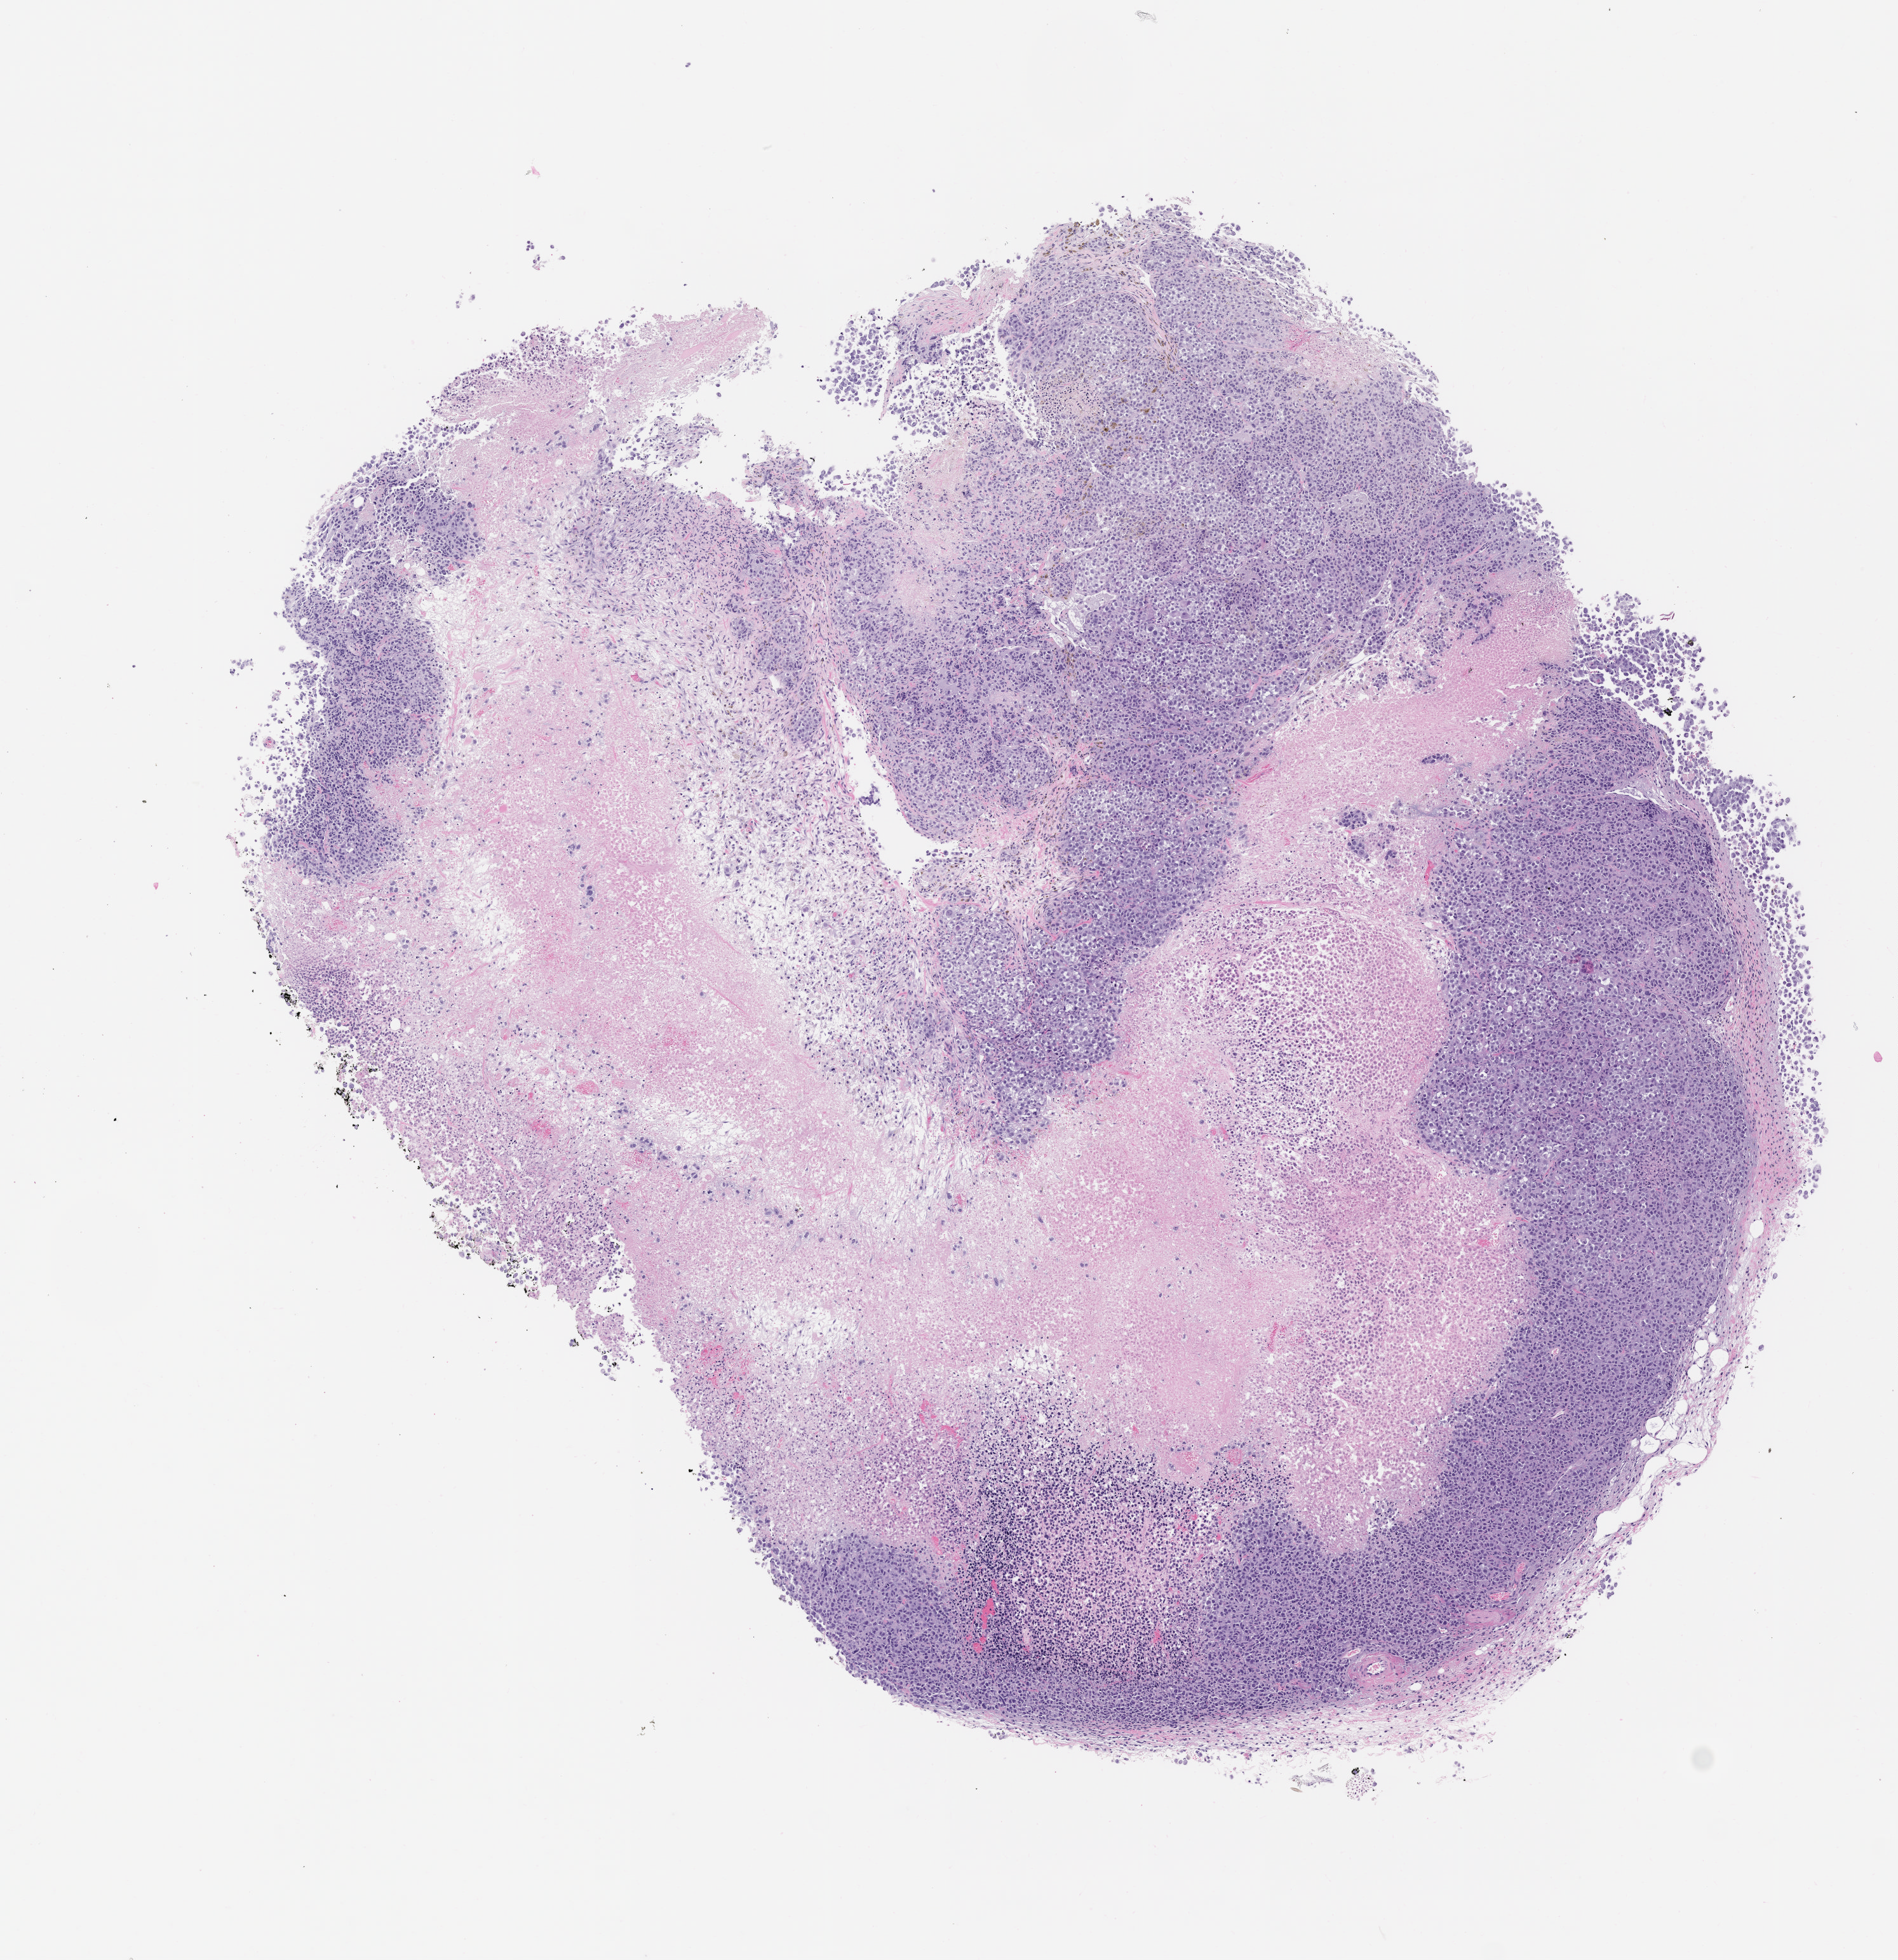
Hematoxylin and eosin (H&E) whole-slide image of a patient-derived xenograft (PDX) tumor grown in a mouse, passage 2, low-resolution overview of the scanned area, about 6.0 x 6.2 mm; formalin-fixed paraffin-embedded section; tumor site category: skin.
Originating patient diagnosis: Melanoma.